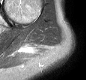
MRI of an extremity soft-tissue mass, one axial slice. Slice 22 of 30 in the series (ordered by position). STIR. MR volume resampled by the dataset authors to the PET/CT grid (not the native acquisition matrix). 86 × 80 image matrix, field of view 84 × 78 mm. Female patient. Case-level facts recorded for this patient, not image findings: histological type: malignant fibrous histiocytoma; grade: low; site of the primary tumour: left arm.
Outlined on this slice (expert contour drawn on MRI and transferred to this co-registered scan by the dataset authors):
- gross tumour volume (mass): box from (x=22, y=47) to (x=29, y=52) px